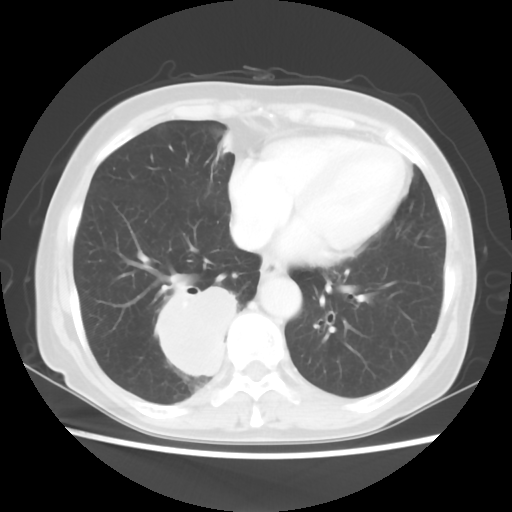
Chest CT, one axial slice; slice 19 of 56 in the series (ordered by position); reconstruction kernel STANDARD; 120 kVp; lung window (W 1500 / L -600 HU); 5 mm slice thickness; 512 × 512 image matrix, field of view 332 × 332 mm. Patient: female, 66 years. From the clinical record (not read from this slice): clinical TNM (as recorded): T2 N3 M0.
Structures marked on this image (rectangle marked by the reading radiologist):
- lung tumour (recorded histology: small cell carcinoma): bounding box (x1, y1, x2, y2) in pixels: (148, 274, 245, 381)